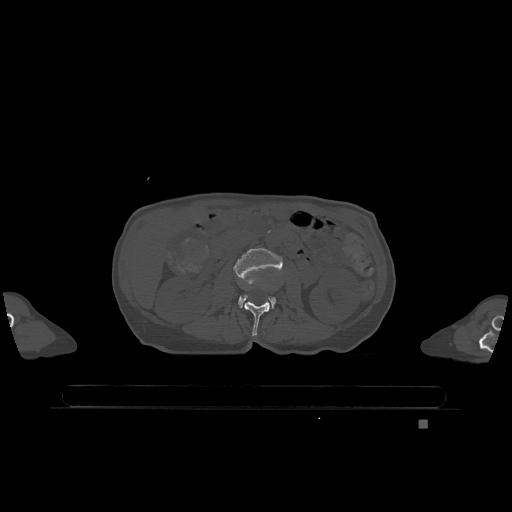
CT including the spine, one axial slice; position 393 of 1317 along the scan axis; bone window (W 1800 / L 400 HU); 512 × 512 image matrix. Female patient, age 74 years. Case-level facts recorded for this patient, not image findings: primary cancer: lung; vertebrae with lytic lesions (as recorded): T1, T4, T5, T6, L4, L5.
Outlined on this slice (semi-automatic segmentation, software-assisted and operator-edited):
- L2 vertebra: bounding box <244,301,270,336> (left, top, right, bottom; pixels)
- L3 vertebra: <234,248,283,308>